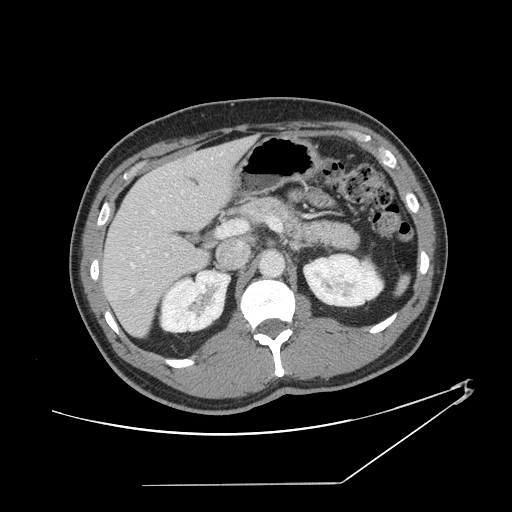
Contrast-enhanced abdominal CT, one axial slice; position 77 of 152 along the scan axis; 120 kVp; soft-tissue window (W 400 / L 40 HU); 2.5 mm slice thickness; 512 × 512 image matrix, field of view 432 × 432 mm. Male patient, age 45 years. From the clinical record (not read from this slice): diagnosis: colorectal cancer liver metastases, imaged before liver resection; multiple liver metastases: no; largest metastasis: 1 cm.
Structures marked on this image (expert manual segmentation):
- hepatic veins: bounding box <131,152,223,292> (left, top, right, bottom; pixels)
- liver: <103,138,253,336>
- planned liver remnant (the part of the liver to remain after resection): <103,158,213,336>
- portal vein (with intrahepatic branches): <131,217,282,268>